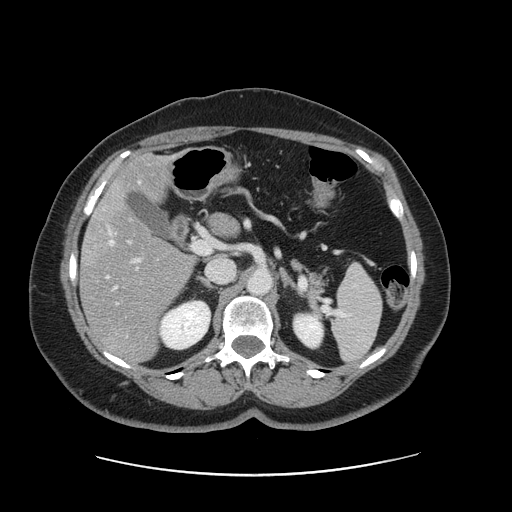
Contrast-enhanced abdominal CT, one axial slice; position 80 of 161 along the scan axis; 120 kVp; intravenous contrast given; soft-tissue window (W 400 / L 40 HU); 512 × 512 image matrix, field of view 398 × 398 mm. Female patient, age 62 years. From the clinical record (not read from this slice): diagnosis: colorectal cancer liver metastases, imaged before liver resection; multiple liver metastases: no; largest metastasis: 2.5 cm; disease in both lobes: no.
Annotated regions visible in this slice (outlined manually by an expert reader):
- hepatic veins: bounding box [x1, y1, x2, y2] px = [107, 181, 141, 289]
- liver: [81, 156, 235, 362]
- planned liver remnant (the part of the liver to remain after resection): [113, 157, 235, 235]
- portal vein (with intrahepatic branches): [128, 240, 140, 262]